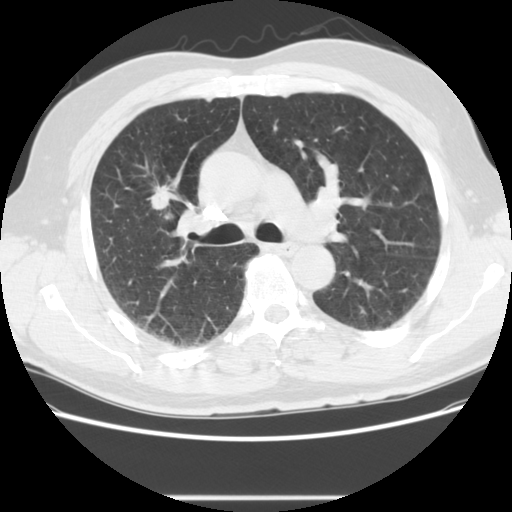
Low-dose screening chest CT, one axial slice. Slice 87 of 139 in the series (ordered by position). Lung window (W 1500 / L -600 HU). 2.5 mm slice thickness. 512 × 512 image matrix, field of view 360 × 360 mm.
Structures marked on this image (outlined manually by an expert reader):
- lesion 1 (tumor, upper lobe of right lung): bounding box <150,184,171,210> (left, top, right, bottom; pixels)